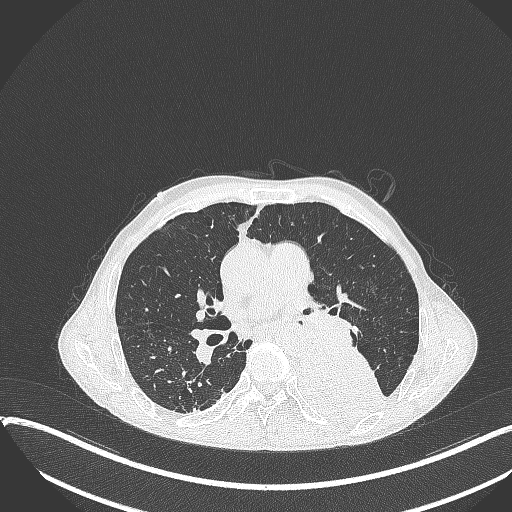
Chest CT, one axial slice; position 207 of 401 along the scan axis; reconstruction kernel B70f; lung window (W 1500 / L -600 HU); 1 mm slice thickness; 512 × 512 image matrix, field of view 400 × 400 mm. Male patient, age 57 years. From the clinical record (not read from this slice): clinical TNM (as recorded): T4 N0 M0.
Annotated regions visible in this slice (rectangle marked by the reading radiologist):
- lung tumour (recorded histology: squamous cell carcinoma): box from (x=293, y=343) to (x=390, y=427) px